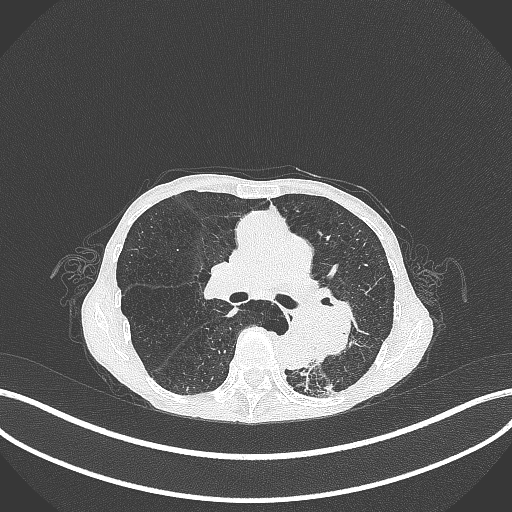
Chest CT, one axial slice. Slice 164 of 347 in the series (ordered by position). 120 kVp. Lung window (W 1500 / L -600 HU). 1 mm slice thickness. 512 × 512 image matrix. Female patient, age 70 years. Case-level facts recorded for this patient, not image findings: clinical TNM (as recorded): T3 N0 M0; histopathological grade: G3.
Outlined on this slice (bounding box drawn by a radiologist):
- lung tumour (recorded histology: small cell carcinoma): box from (x=289, y=299) to (x=360, y=358) px